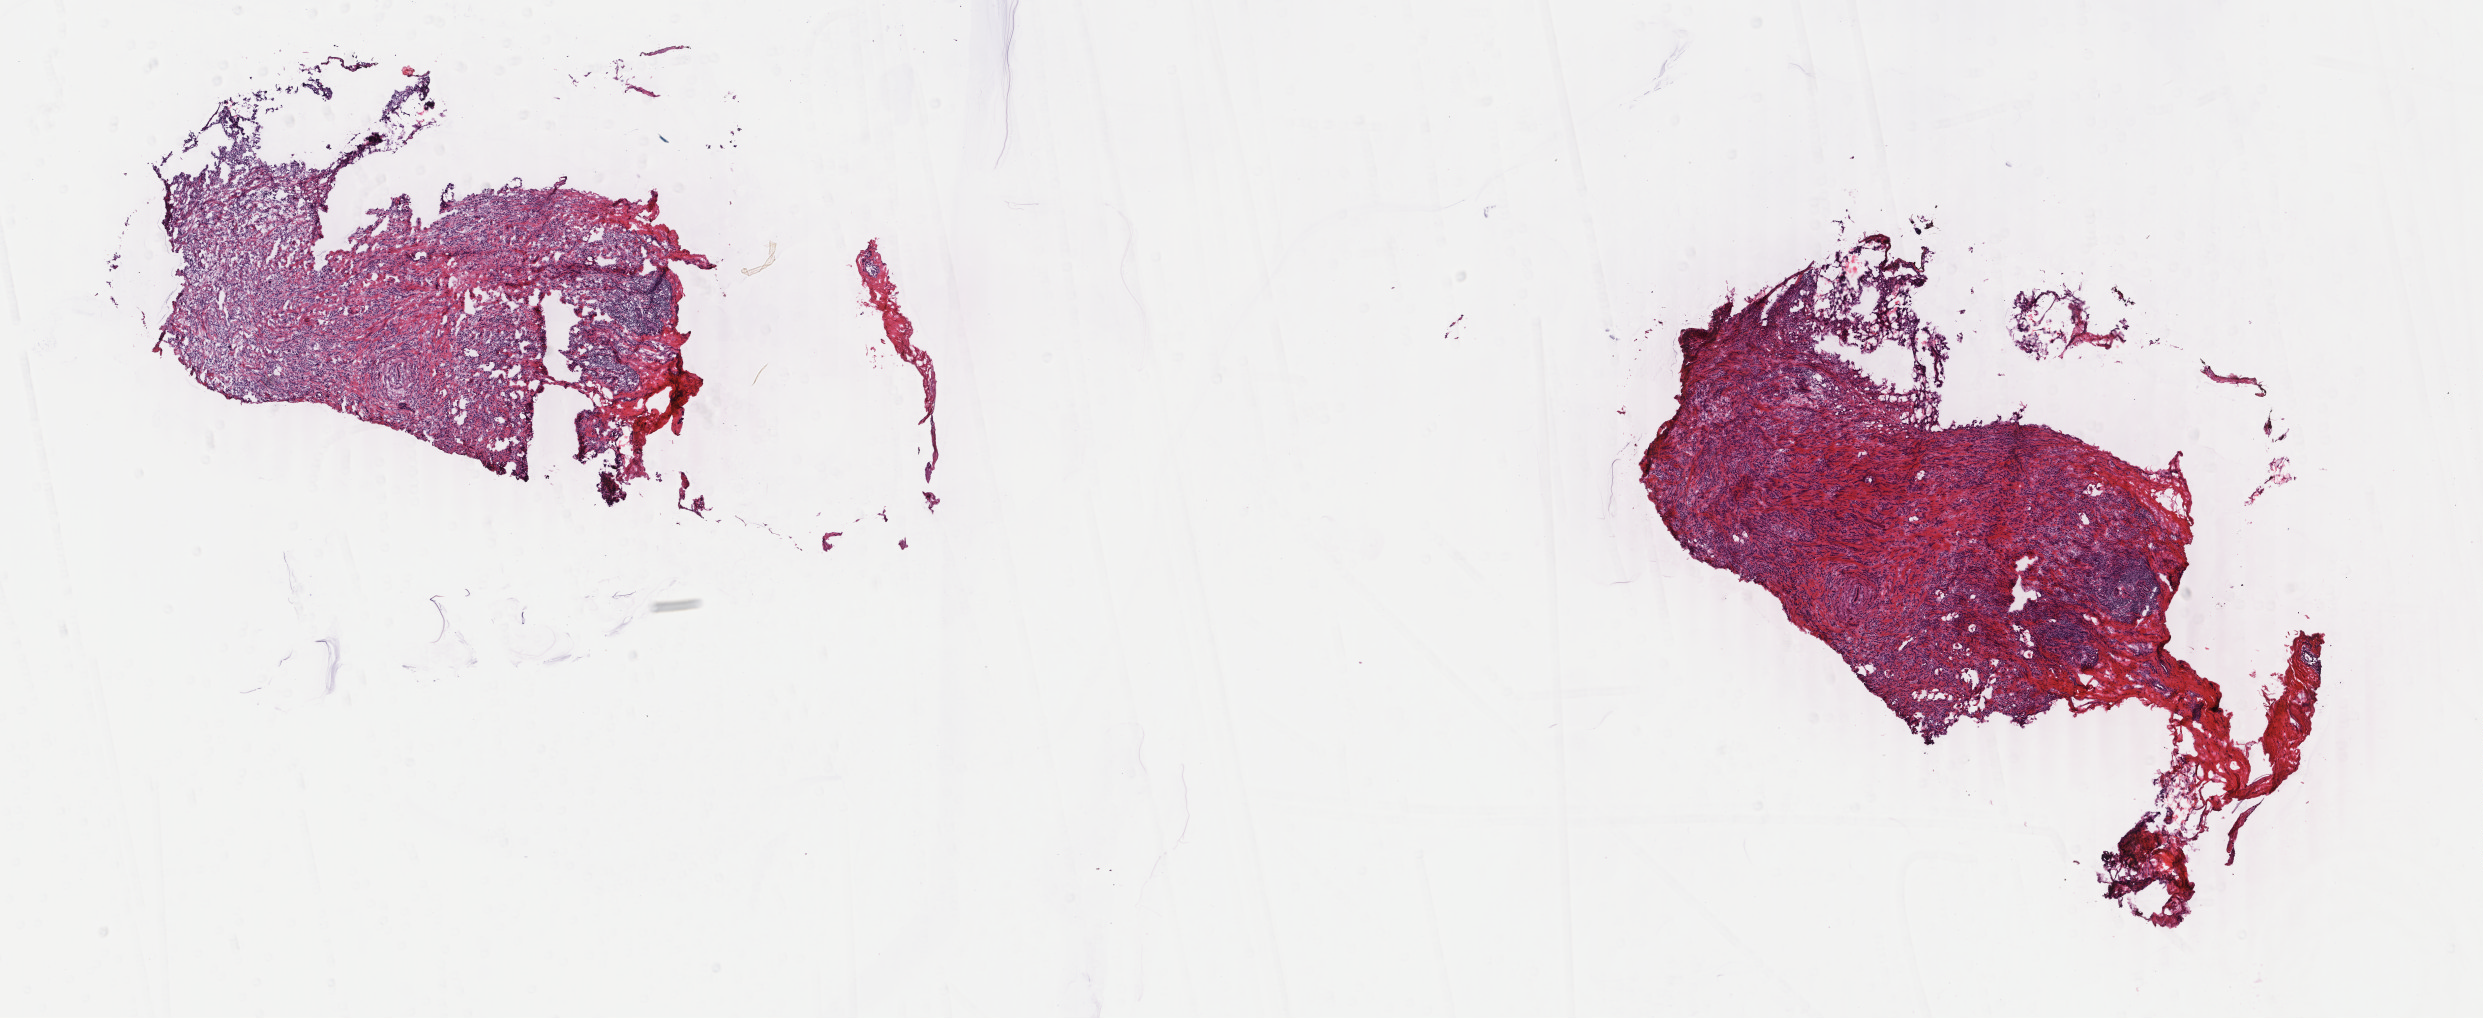
Digitized H&E tissue section (whole slide), shown as a low-resolution overview of the whole scanned area (about 19.8 x 8.1 mm); frozen section; primary tumour sample from the breast. Female, age 70 years at initial diagnosis. Pathologist review of this section (percent, as recorded): tumour cells 85%, tumour nuclei 85%, normal cells 1%, stromal cells 14%, necrosis 0%. Infiltration values recorded for this section: lymphocyte infiltration 1%, monocyte infiltration 0%, neutrophil infiltration 0%.
Laterality: right. Lymph nodes positive (case pathology): 0 of 4 examined. AJCC pathologic stage: IIA (6th edition). Diagnosis: Lobular carcinoma, NOS.